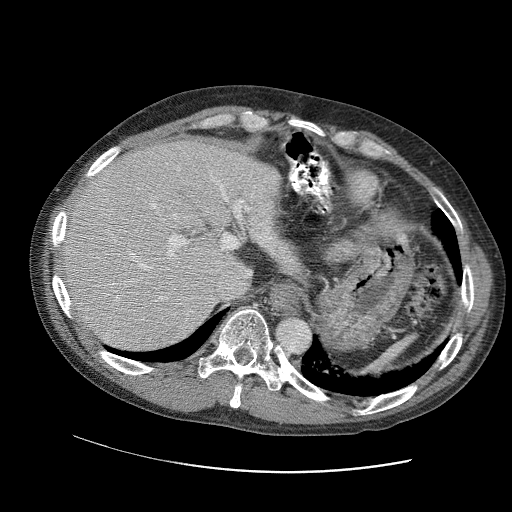
Contrast-enhanced abdominal CT (liver protocol), one axial slice; position 77 of 109 along the scan axis; 120 kVp; soft-tissue window (W 400 / L 40 HU); 2.5 mm slice thickness; 512 × 512 image matrix, field of view 400 × 400 mm. From the clinical record (not read from this slice): diagnosis: hepatocellular carcinoma (patient treated with transarterial chemoembolisation; whether this scan precedes or follows treatment is not stated here); TNM stage (as recorded): Stage-IIIC.
Structures marked on this image (semi-automatic segmentation, software-assisted and operator-edited):
- abdominal aorta: bounding box <278,317,310,351> (left, top, right, bottom; pixels)
- liver parenchyma outside the tumour (the mass and vessels are separate outlines, so this box may not span the whole liver): <56,136,290,350>
- liver vessels: <64,155,268,339>